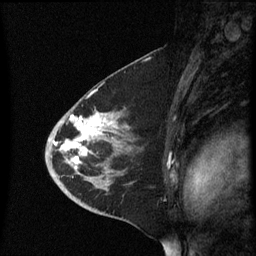
Breast MRI (dynamic contrast-enhanced), one sagittal slice. Position 36 of 60 along the scan axis. Dynamic contrast-enhanced series, image 2 of 3 at this slice position (ordered by acquisition). 1.5 T. TE 4.2 ms, TR 8.4 ms. 2.3 mm slice thickness. 256 × 256 image matrix, field of view 200 × 200 mm. Female patient, age 46 years. Case-level facts recorded for this patient, not image findings: setting: breast cancer imaged before/during neoadjuvant chemotherapy; receptor status: HER2-positive.
Structures marked on this image (semi-automatically segmented with operator editing):
- analysis volume of interest (the breast-tissue region the enhancement analysis was run in; not a lesion): bounding box <45,96,143,187> (left, top, right, bottom; pixels)
- tumour enhancement mask (voxels above the 70 % enhancement threshold inside the analysis volume of interest): <53,112,115,169>